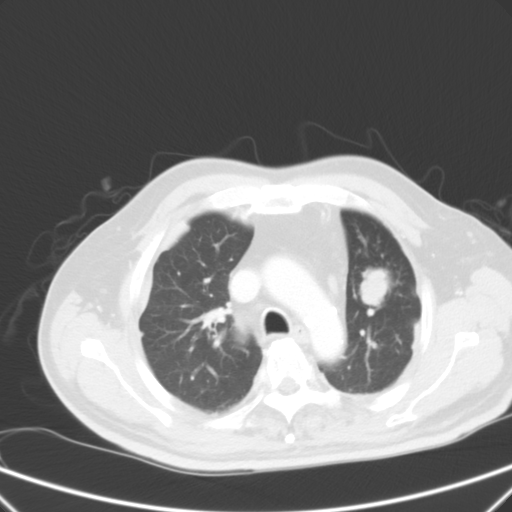
Chest CT, one axial slice. Slice 43 of 59 in the series (ordered by position). 120 kVp. Intravenous contrast given. Lung window (W 1500 / L -600 HU). 512 × 512 image matrix, field of view 357 × 357 mm. Patient: male, 66 years. From the clinical record (not read from this slice): clinical TNM (as recorded): T1c N3 M1a.
Structures marked on this image (bounding box drawn by a radiologist):
- lung tumour (recorded histology: squamous cell carcinoma): box from (x=354, y=262) to (x=397, y=314) px